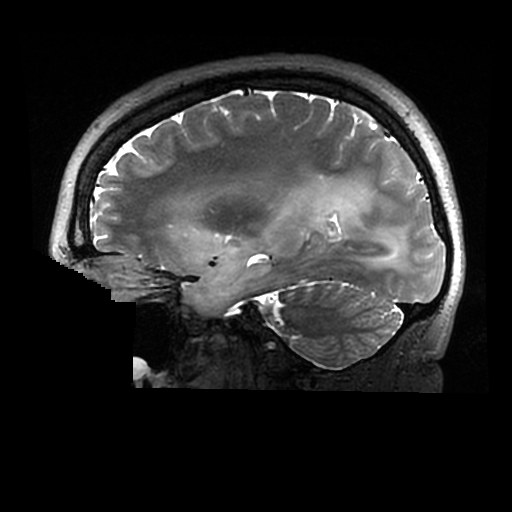
Brain MRI from a brain-tumour surgery series, one sagittal slice. Slice 190 of 320 in the series (ordered by position). 0.6 mm slice thickness. 512 × 512 image matrix, field of view 240 × 240 mm. Case-level facts recorded for this patient, not image findings: histopathology: Astrocytoma; WHO grade: 2; IDH mutation: yes.
Annotated regions visible in this slice (manually delineated by an expert):
- tumour: bounding box (x1, y1, x2, y2) in pixels: (173, 183, 407, 313)